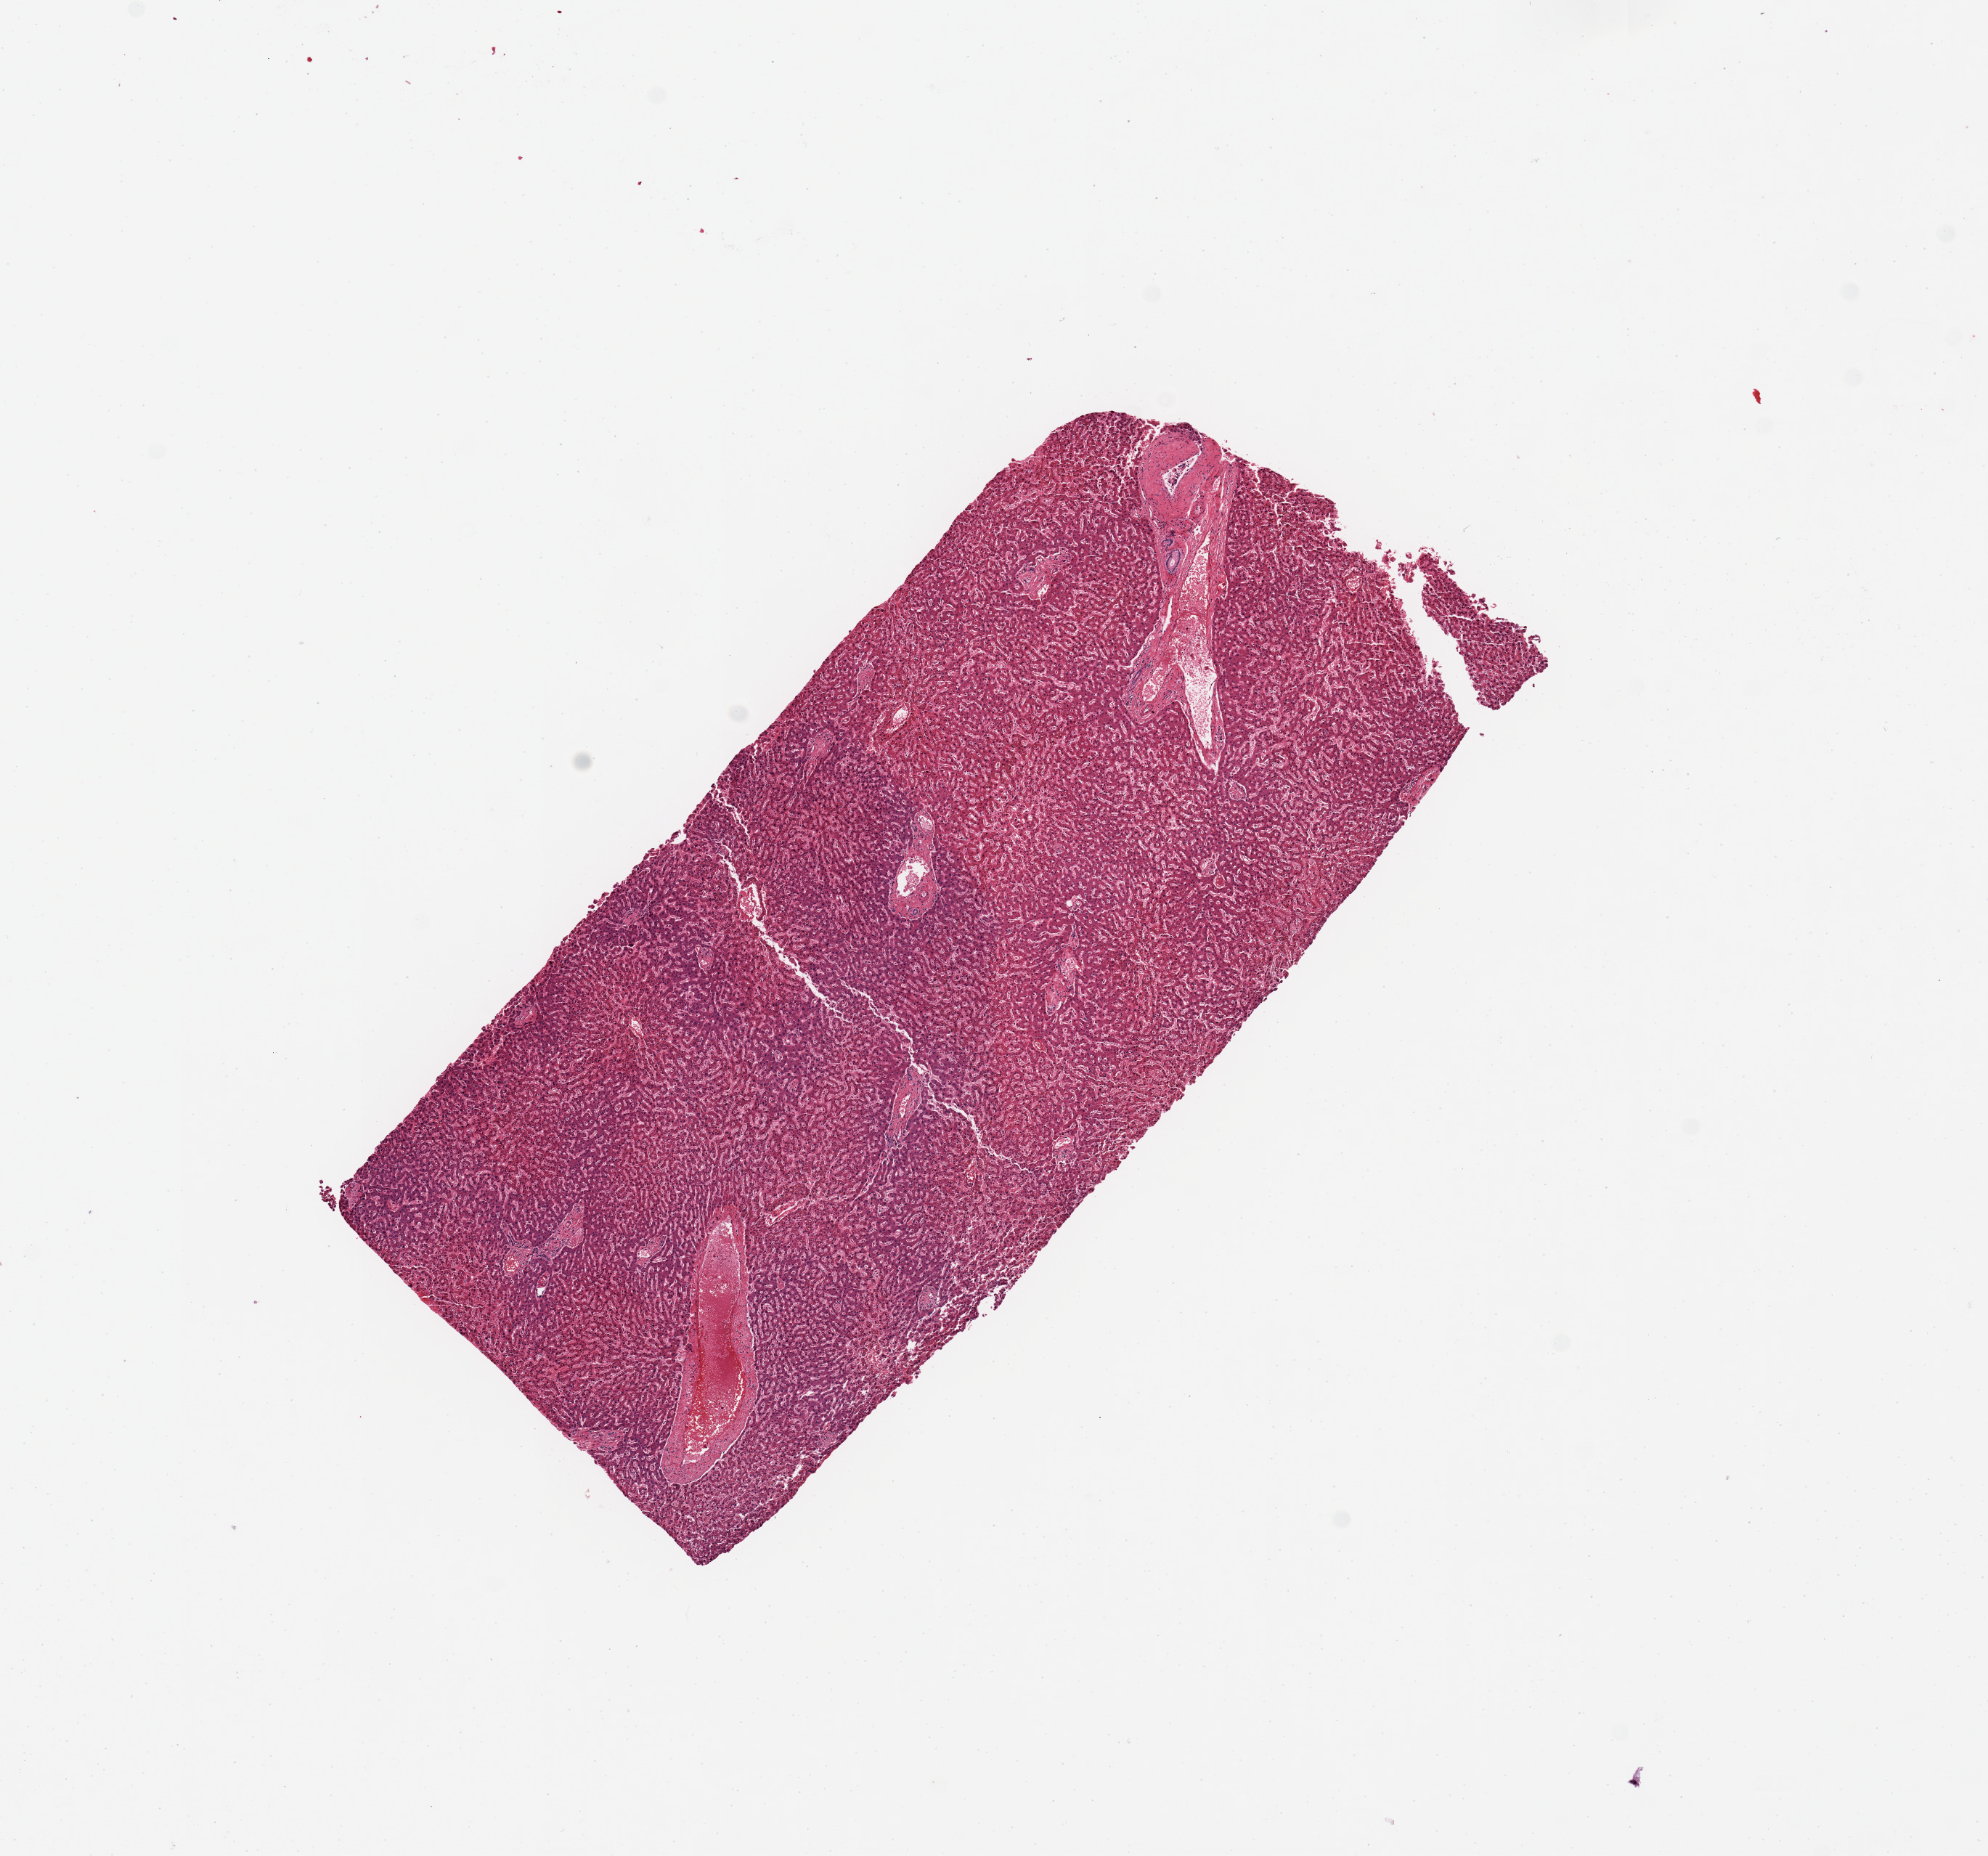
Digitized H&E-stained section, shown as a low-resolution overview of the whole scanned area (about 10.8 x 10.1 mm, slide scanned at 20x); PAXgene-fixed paraffin-embedded (PFPE) section; section of liver (target tissue); donor tissue sample. Male donor.
Reviewer comment on this tissue sample: 1 pieces; liver, not skin.